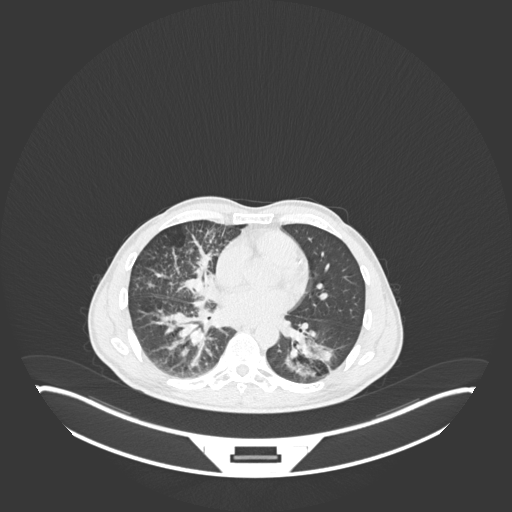
Chest CT, one axial slice; reconstruction kernel B30f; 120 kVp; lung window (W 1500 / L -600 HU); 1 mm slice thickness; 512 × 512 image matrix, field of view 500 × 500 mm. Male patient, age 49 years. Case-level facts recorded for this patient, not image findings: clinical TNM (as recorded): T2b N1 M0.
Structures marked on this image (rectangle marked by the reading radiologist):
- lung tumour (recorded histology: adenocarcinoma): bounding box <285,330,344,382> (left, top, right, bottom; pixels)